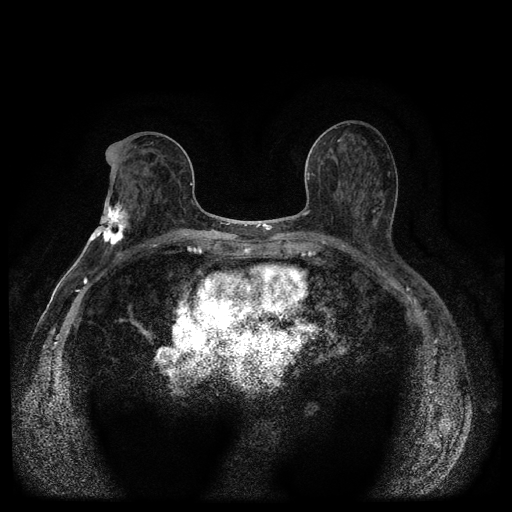
Breast MRI (dynamic contrast-enhanced, multi-phase), one axial slice. Position 54 of 116 along the scan axis. Dynamic contrast-enhanced series, time point 2 of 5 at this slice position (early post-contrast). 1.5 T. TE 2.7 ms, TR 5.4 ms. 2 mm slice thickness. 512 × 512 image matrix, field of view 340 × 340 mm. Female patient, age 75 years.
Annotated regions visible in this slice (semi-automatic segmentation, software-assisted and operator-edited):
- breast lesion (labelled 'tumour' in the annotation; benign lesions carry a separate 'benign' label): bounding box <88,197,129,249> (left, top, right, bottom; pixels)